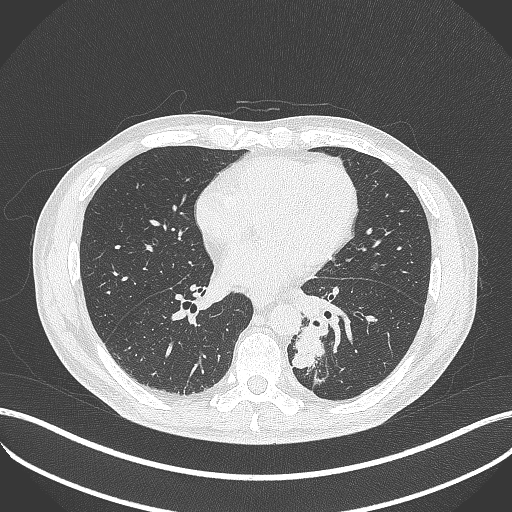
Chest CT, one axial slice; reconstruction kernel B70f; 120 kVp; lung window (W 1500 / L -600 HU); 1 mm slice thickness; 512 × 512 image matrix. Male patient, age 72 years. Case-level facts recorded for this patient, not image findings: clinical TNM (as recorded): T2b N0 M1.
Outlined on this slice (bounding box drawn by a radiologist):
- lung tumour (recorded histology: adenocarcinoma): bounding box <292,319,326,377> (left, top, right, bottom; pixels)